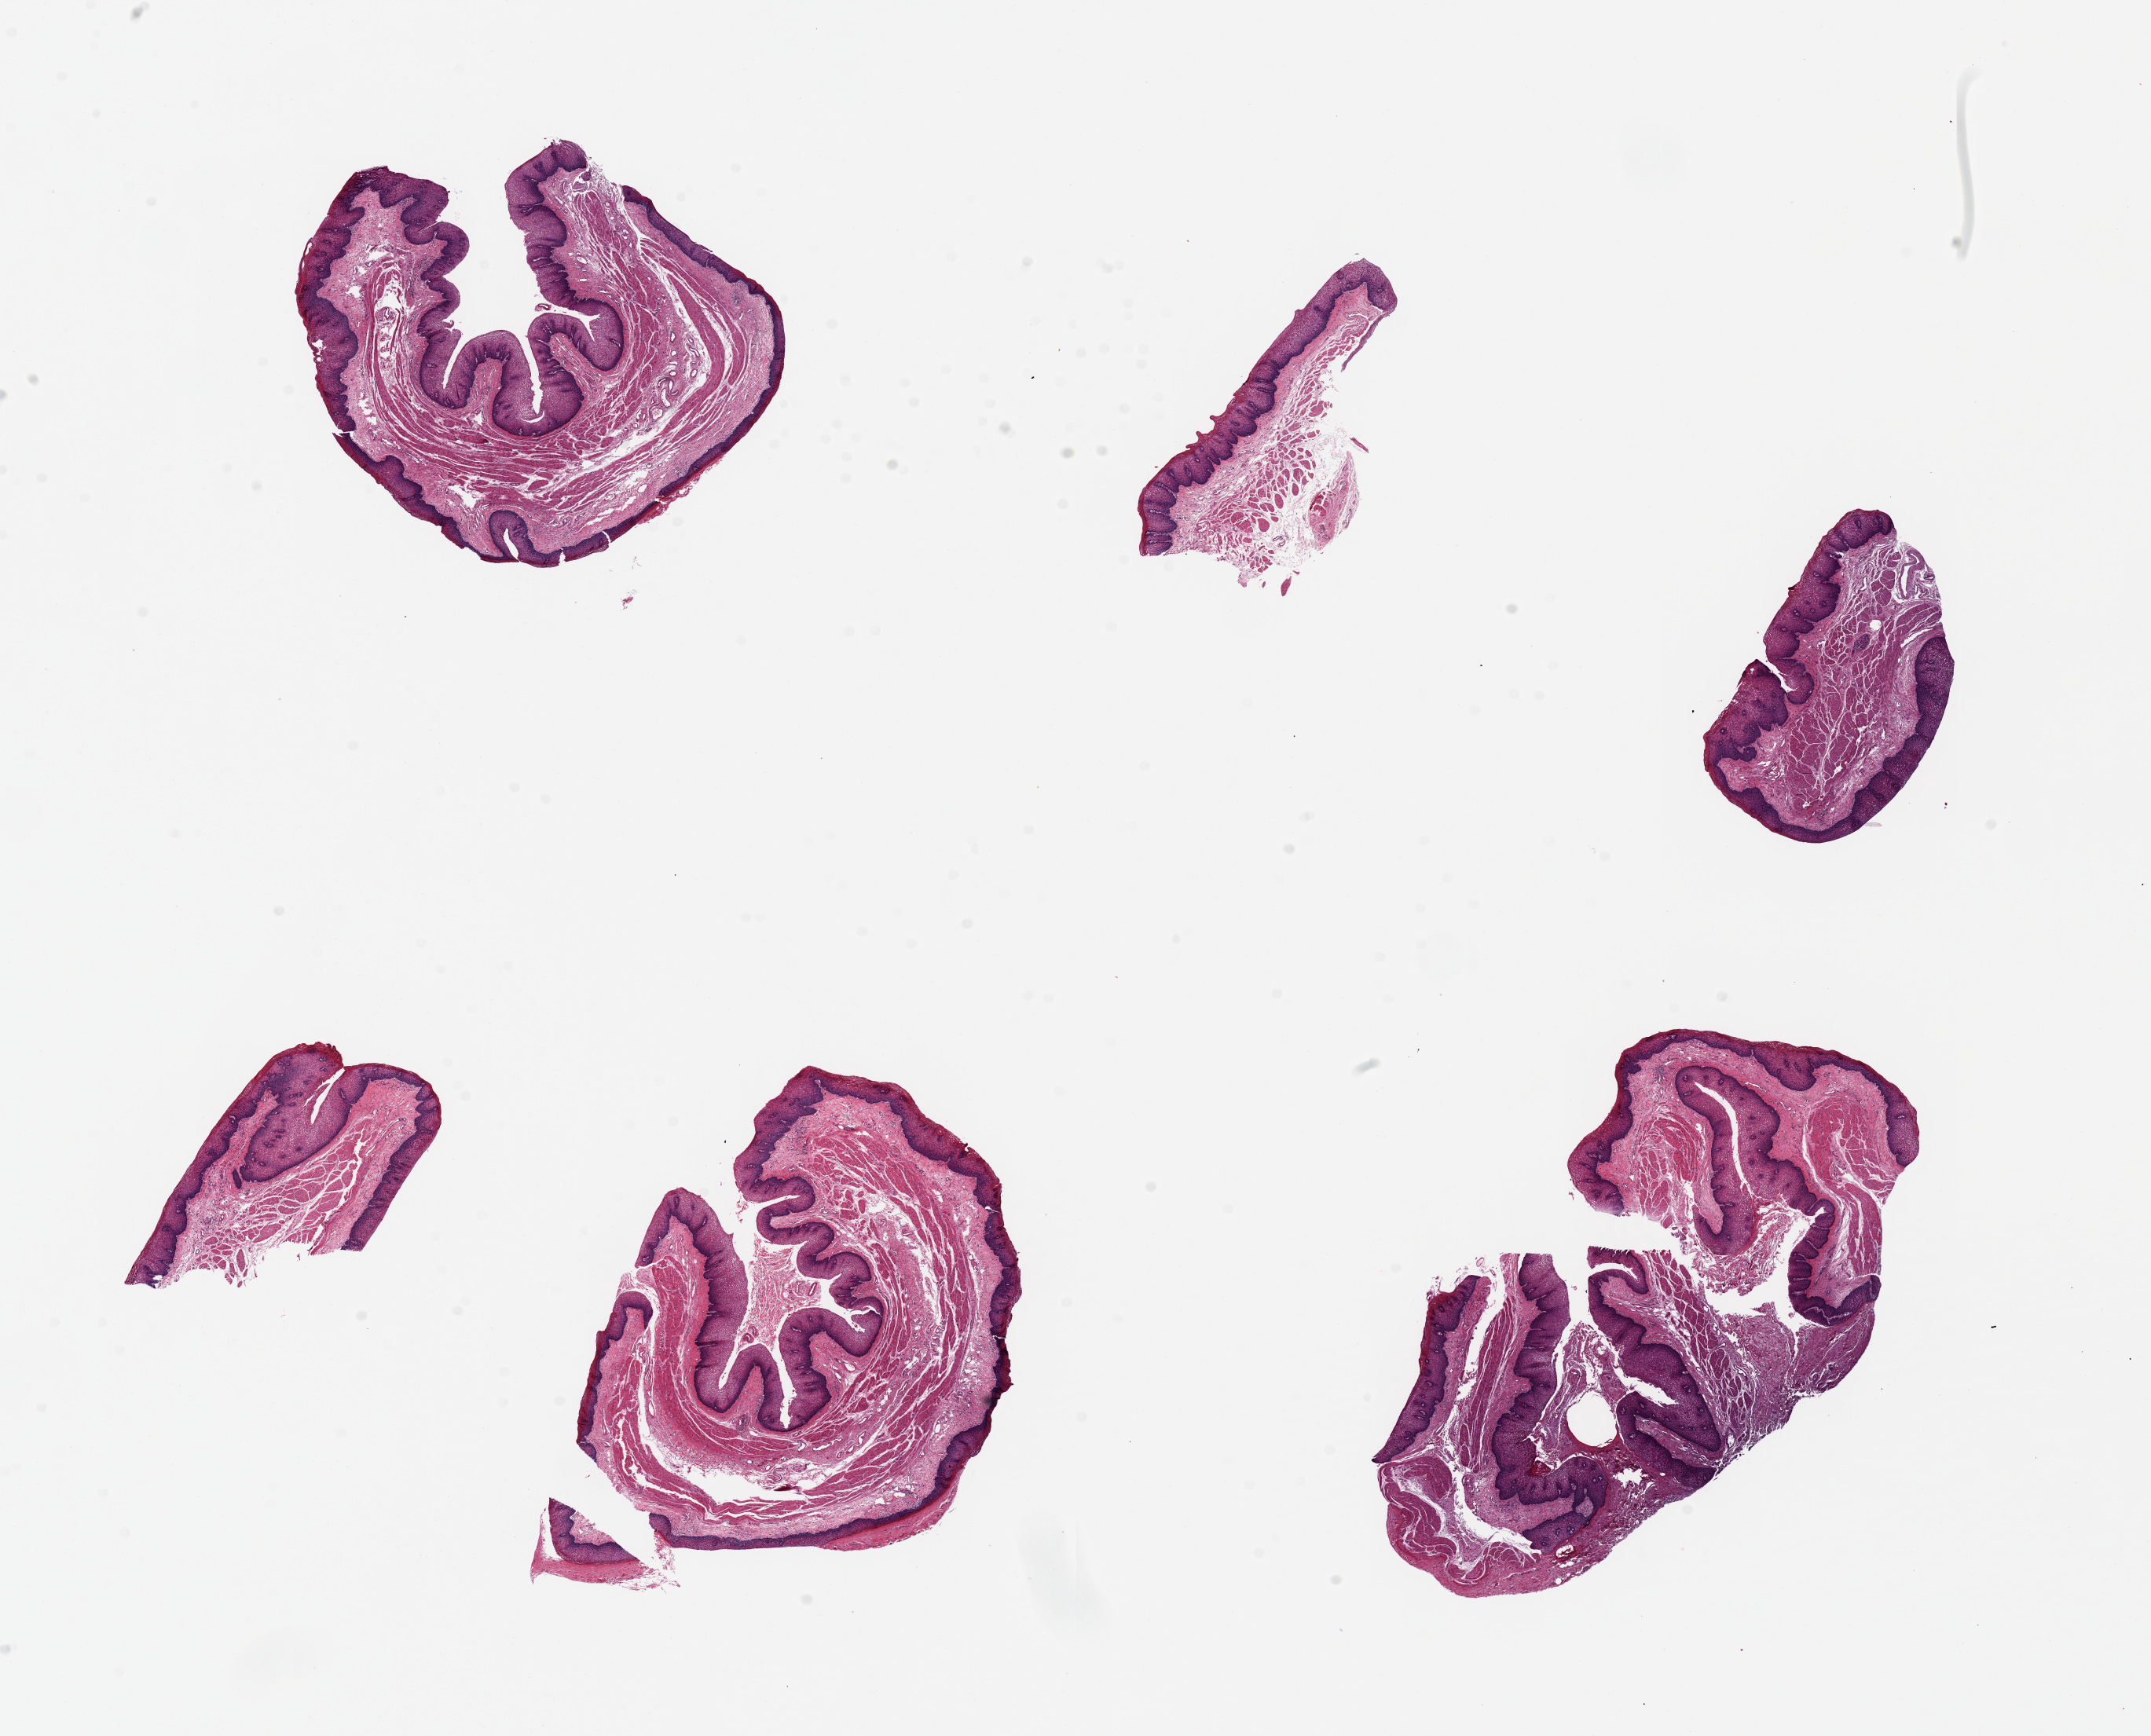
Hematoxylin and eosin (H&E) whole-slide image — shown as a low-resolution overview of the whole scanned area (about 21.7 x 17.5 mm). PAXgene-fixed paraffin-embedded (PFPE) section. Section of esophageal mucous membrane (target tissue). Donor tissue sample. Donor: female.
Reviewer comment on this tissue sample: 6 pieces ~5x4mm. Squamous mucosa well preserved, about ~20 total volume (fragments are enfolded).